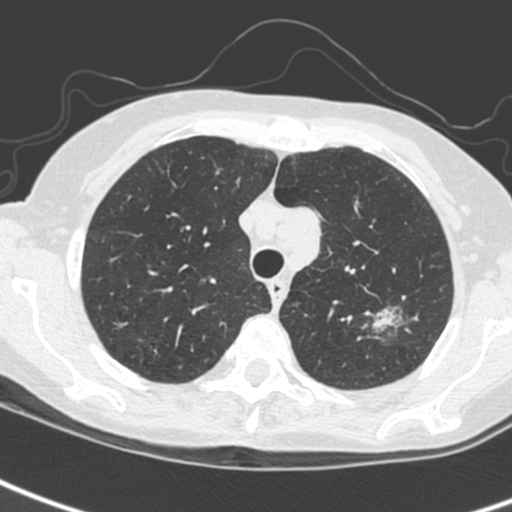
Chest CT (low-dose screening protocol), one axial image; baseline annual screen; lung window (W 1500 / L -600 HU); 1.3 mm slice thickness; 120 kVp; slice 42 of 242 in the series. Female, age 61 years at enrolment. Current smoker at enrolment.
- Lesion marked by an expert reader, bounding box <350,300,412,350> (left, top, right, bottom; pixels).
- The screening reader recorded 2 non-calcified nodules or masses ≥4 mm on this exam; which of them this box marks is not recorded.
- Official screen result: positive, change unspecified: nodule(s) >= 4 mm or enlarging nodule(s), mass(es), or other non-specific abnormalities suspicious for lung cancer.
- Later outcome: lung cancer diagnosed 29 days after this screen — small cell carcinoma, NOS, left upper lobe, stage IV (AJCC 6th edition).